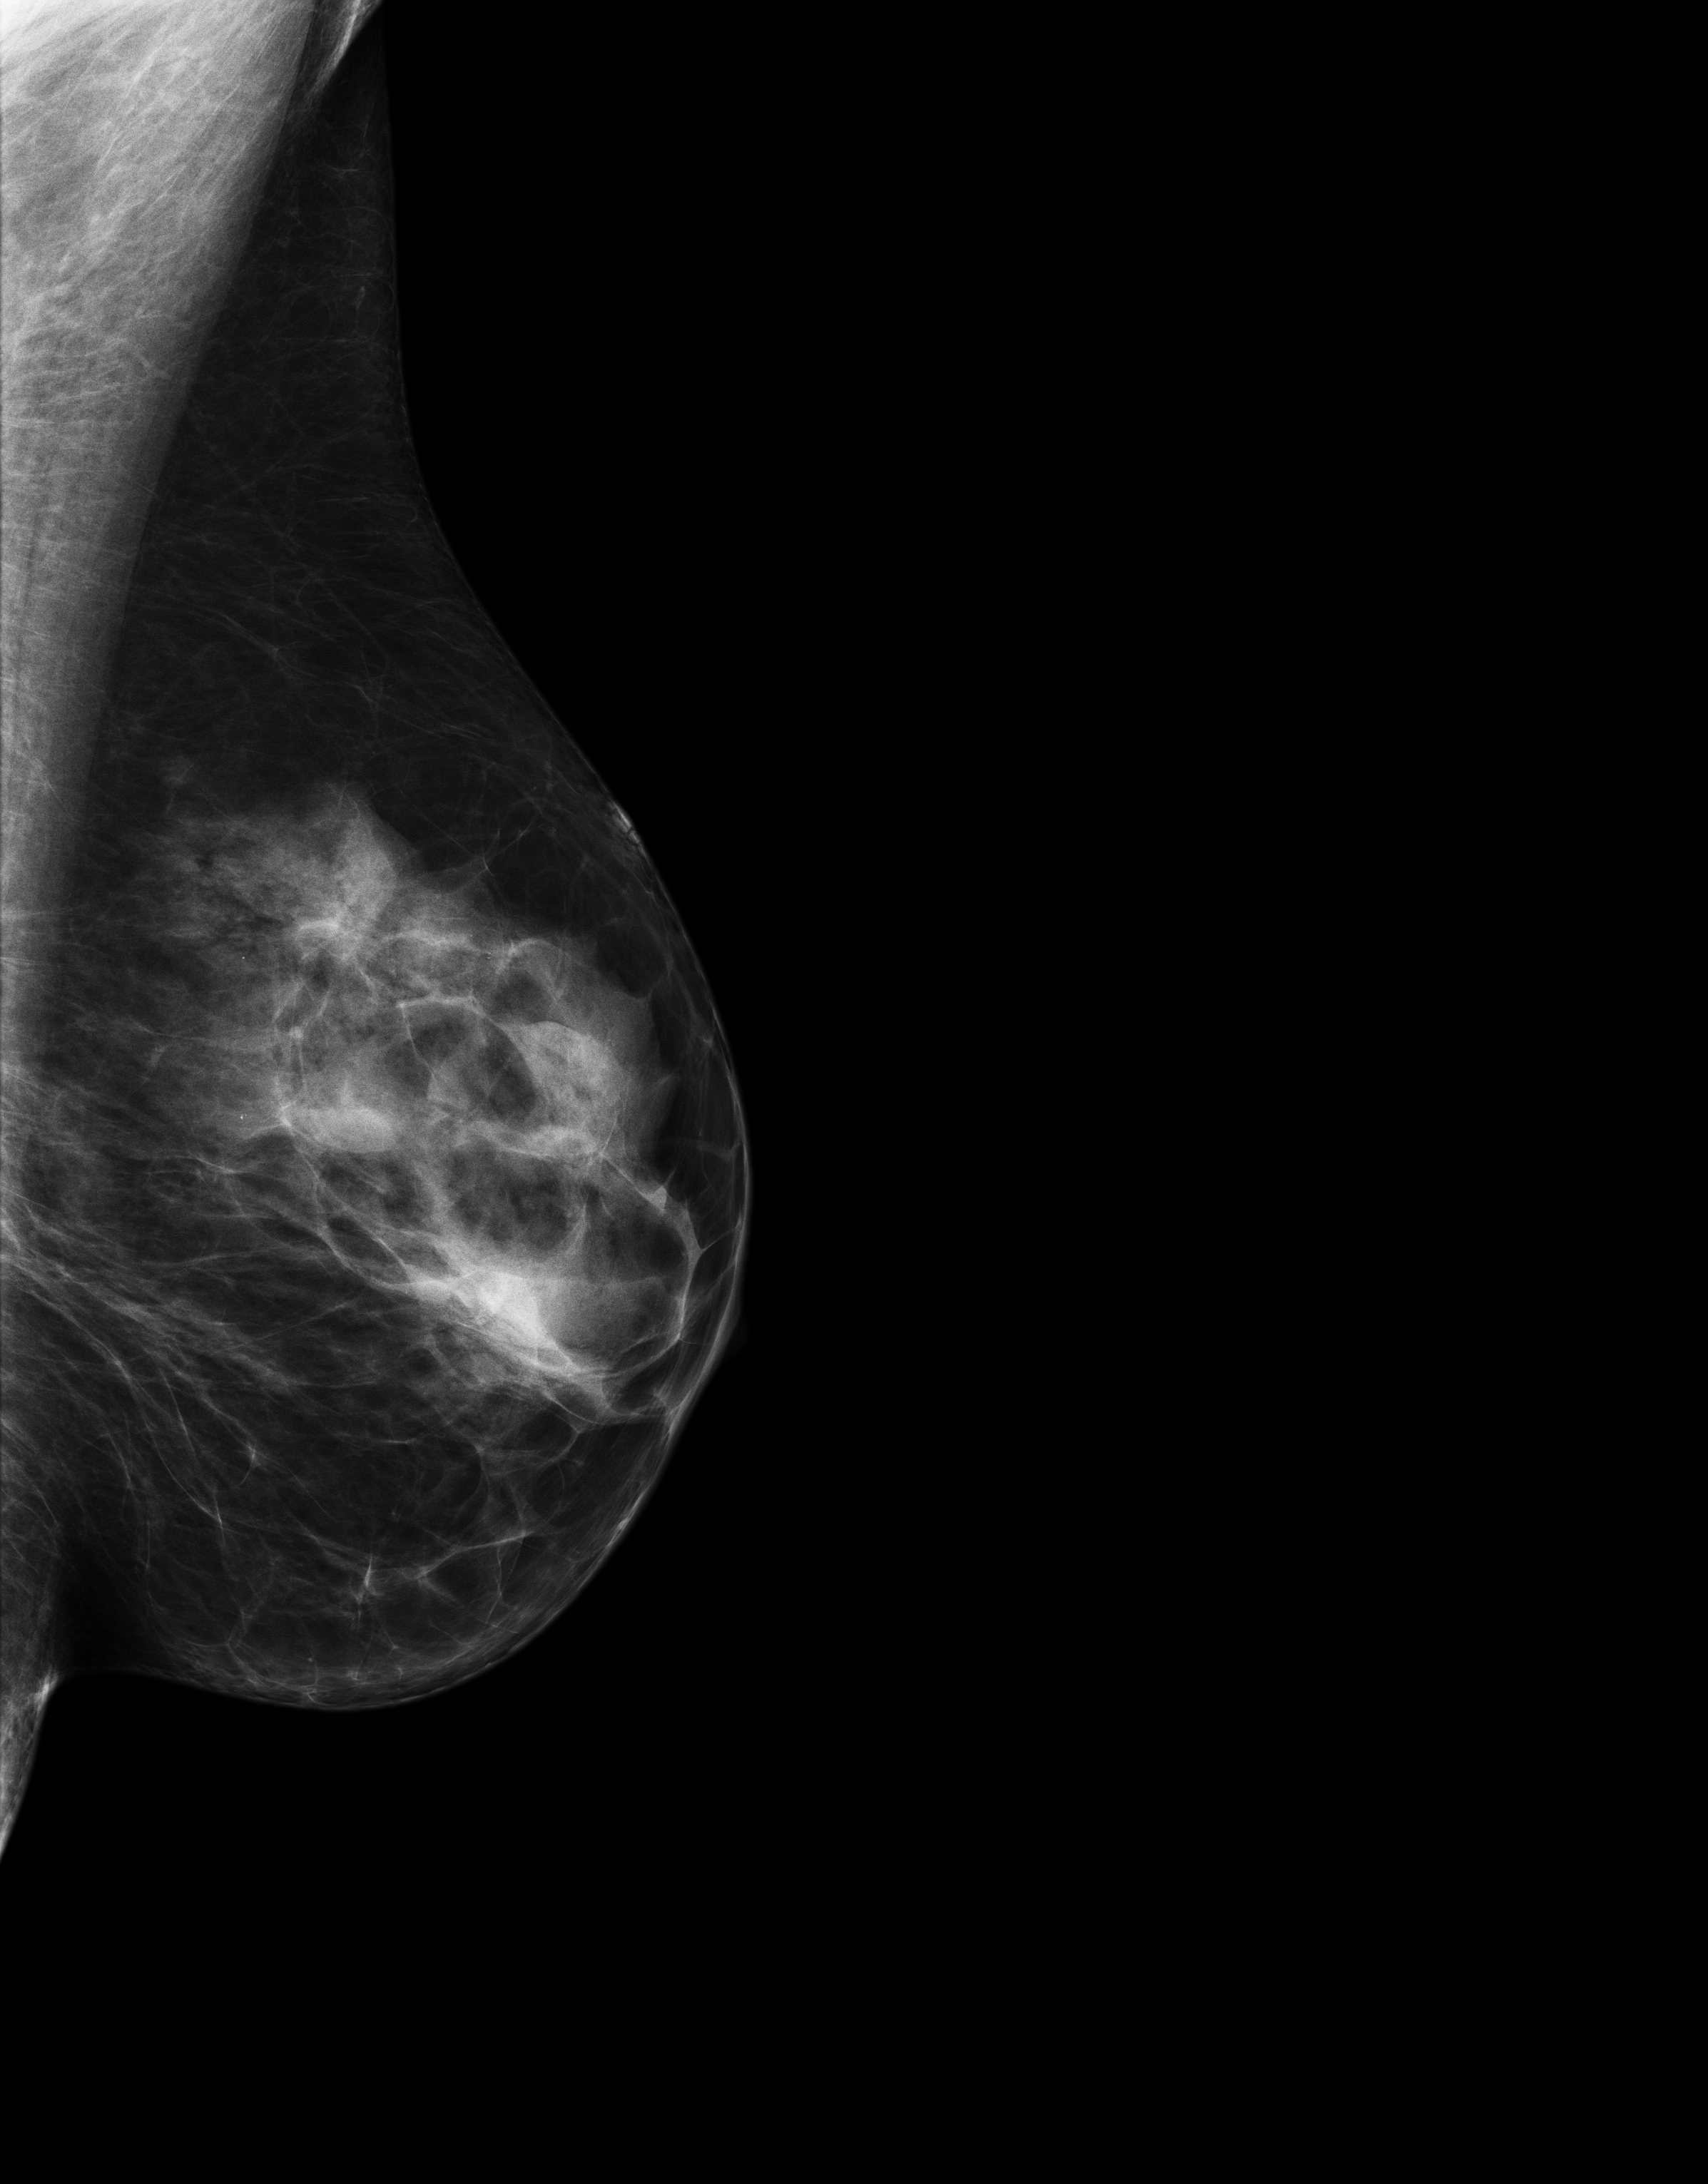
Annual screening mammography examination. Patient: female, 52 years.
Image type: full-field digital mammogram. Breast: left. Projection: medio-lateral oblique projection.